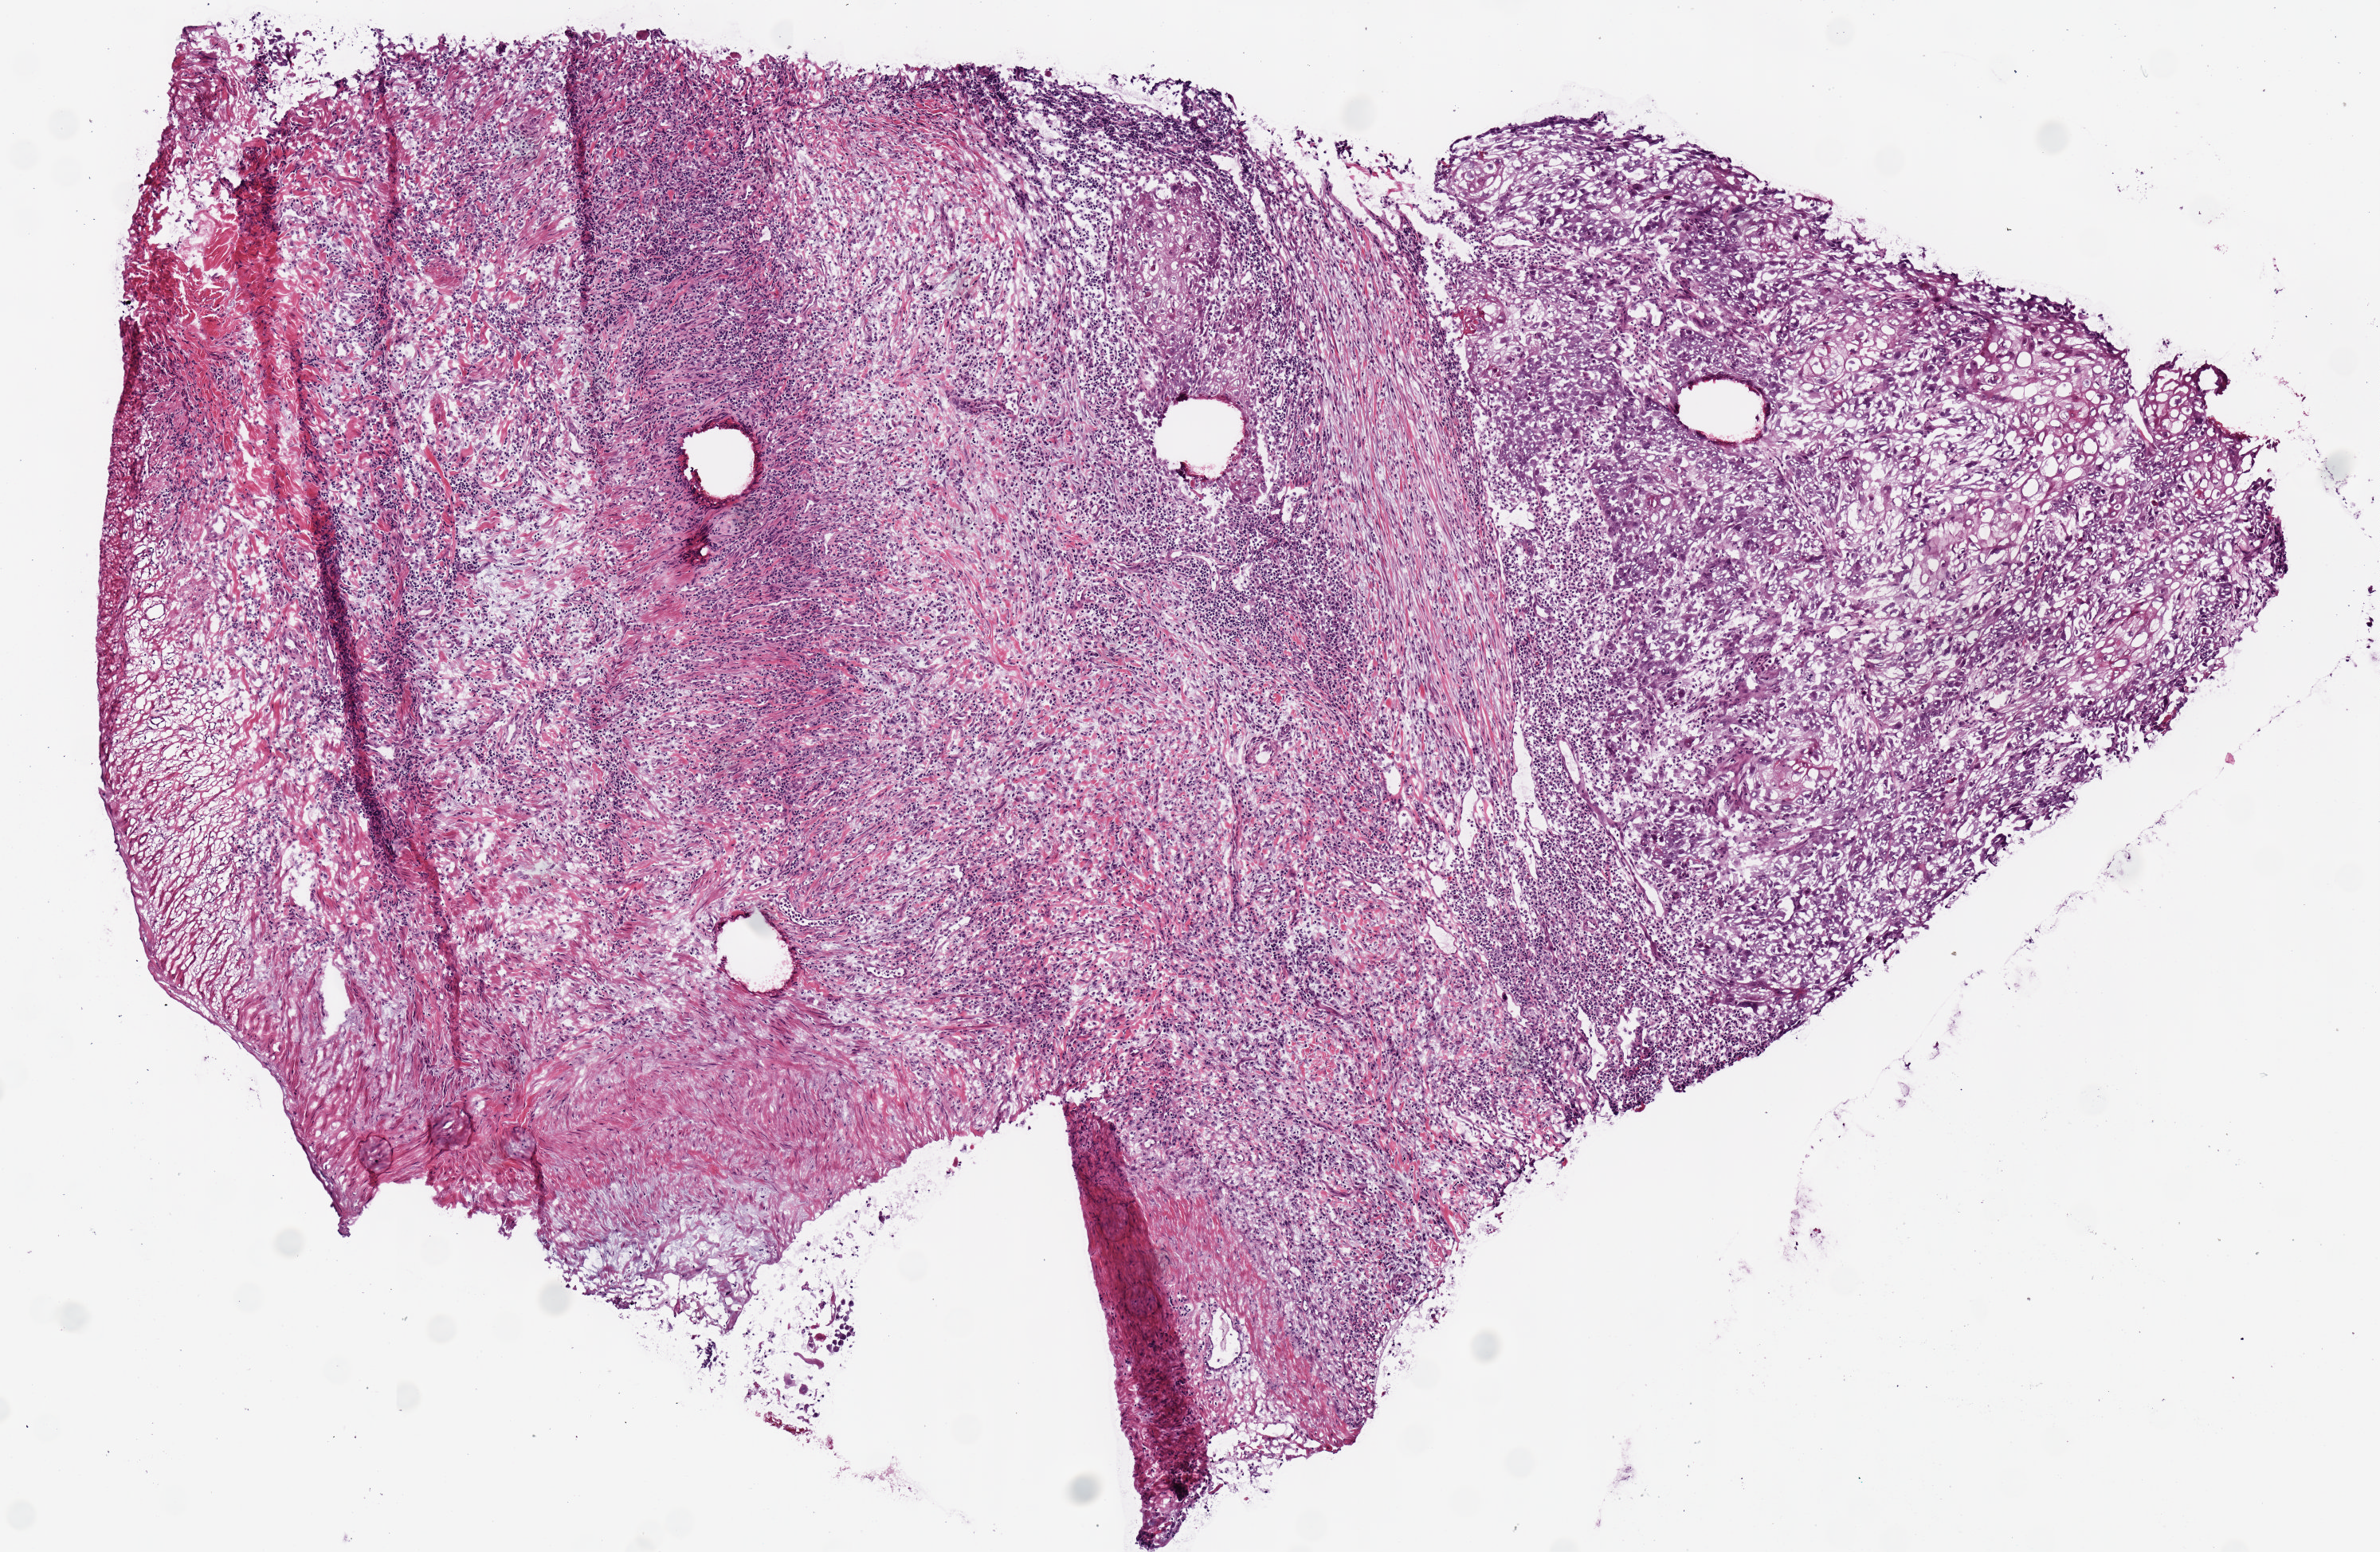
Digitized H&E tissue section (whole slide), shown as a low-resolution overview of the whole scanned area (about 5.9 x 3.8 mm, slide scanned at 20x). Frozen section from the bottom of the tissue portion. Primary tumour sample from the lung. Male patient; age at initial diagnosis 70 years.
TNM: T2 N0 M0. AJCC pathologic stage: IB (6th edition). Pathologic diagnosis: Squamous cell carcinoma, NOS (upper lobe, lung).